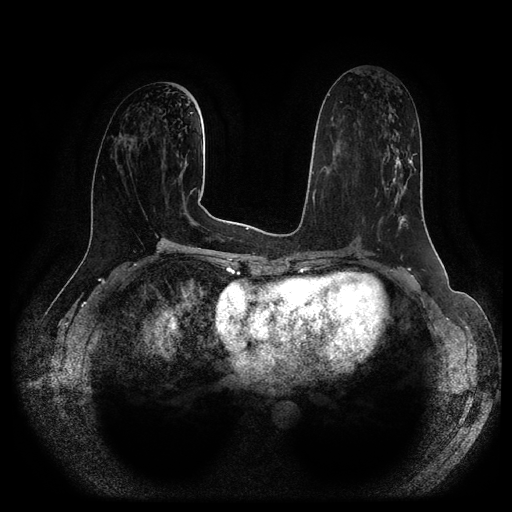
Breast MRI (dynamic contrast-enhanced, multi-phase), one axial slice; position 50 of 116 along the scan axis; dynamic contrast-enhanced series, time point 2 of 5 at this slice position (early post-contrast); 1.5 T; TE 2.6 ms, TR 5.2 ms; 512 × 512 image matrix, field of view 380 × 380 mm. Female patient, age 57 years.
Outlined on this slice (semi-automatic segmentation, software-assisted and operator-edited):
- breast lesion (labelled 'tumour' in the annotation; benign lesions carry a separate 'benign' label): bounding box (x1, y1, x2, y2) in pixels: (381, 143, 416, 207)